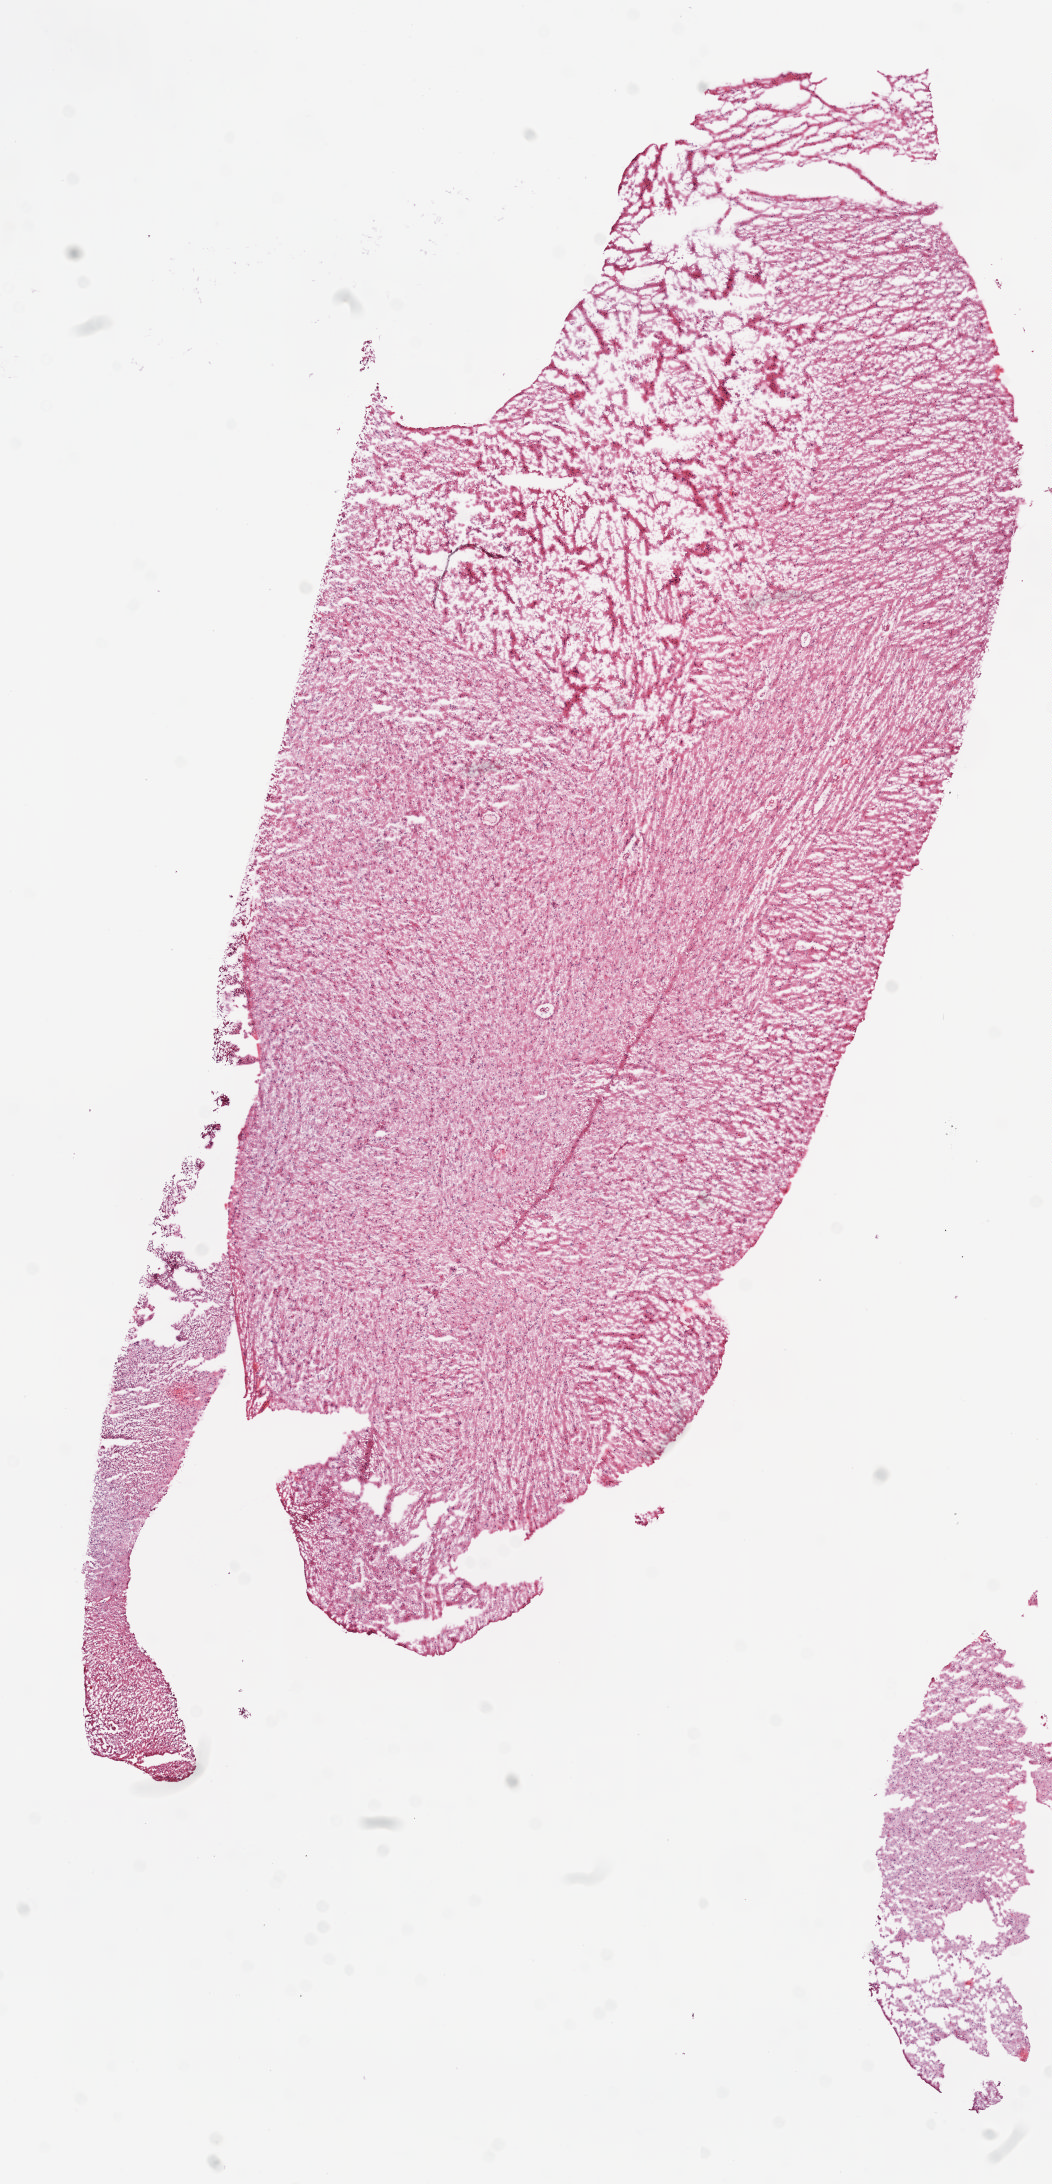
Whole-slide histology image, Hematoxylin and eosin (H&E) stained, whole scanned area (about 8.4 x 17.5 mm, slide scanned at 5x) shown as a low-resolution overview, frozen section from the top of the tissue portion, brain, primary tumour sample. Female patient; age at initial diagnosis 54 years. Histologic grade: G3 (poorly differentiated). Pathologist review of this section (percent, as recorded): tumour cells 100%, tumour nuclei 70%, normal cells 0%, stromal cells 0%, necrosis 0%.
Laterality: left. Diagnosis: Astrocytoma, anaplastic.